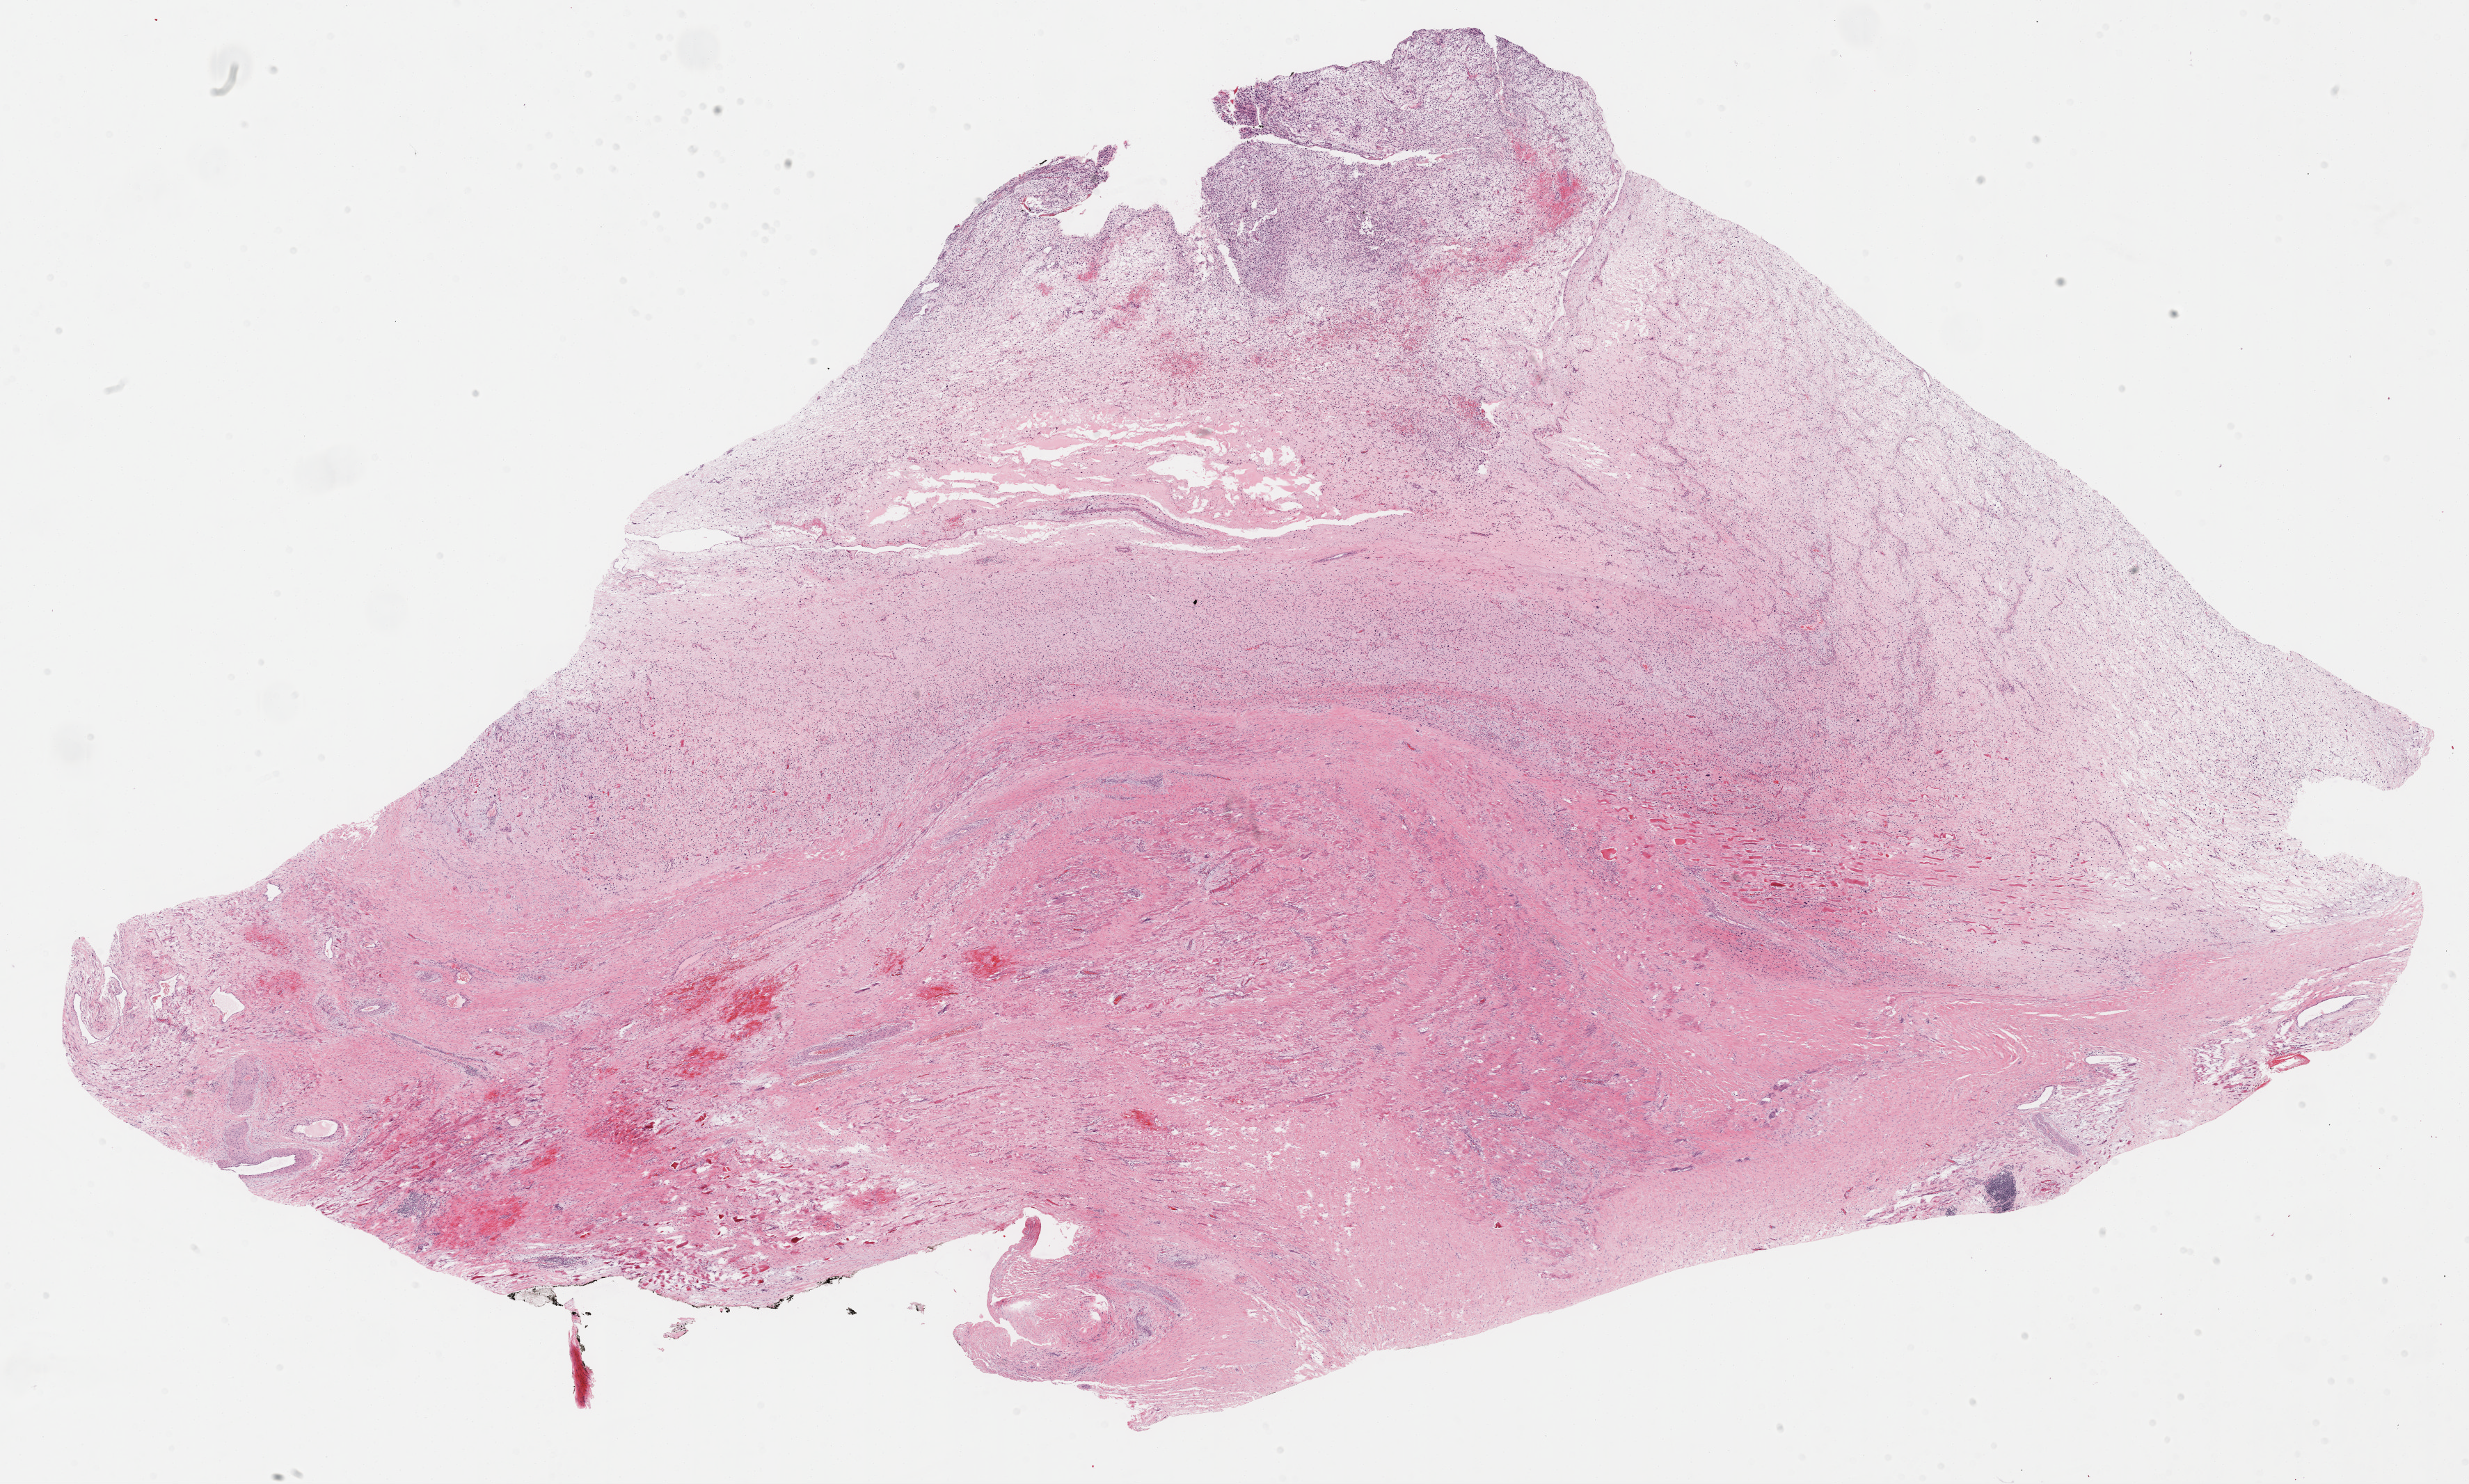
H&E whole-slide image, shown as a low-resolution overview of the whole scanned area (about 28.7 x 17.2 mm); FFPE section; sample: primary tumour, retroperitoneum and peritoneum. Patient: male, age at initial diagnosis 57 years.
Diagnosis: Fibromyxosarcoma (retroperitoneum).